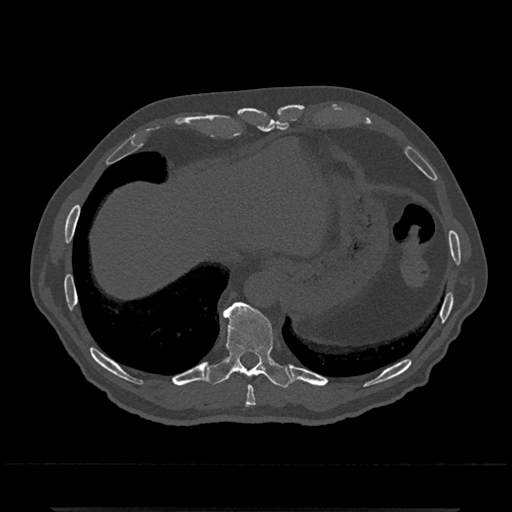
CT including the spine, one axial slice; reconstruction kernel Br40s/3; bone window (W 1800 / L 400 HU); 0.5 mm slice thickness; 512 × 512 image matrix, field of view 393 × 393 mm. Male patient, age 67 years. Case-level facts recorded for this patient, not image findings: primary cancer: prostate.
Structures marked on this image (semi-automatic segmentation, software-assisted and operator-edited):
- T10 vertebra: bounding box <205,302,292,388> (left, top, right, bottom; pixels)
- T9 vertebra: <245,386,256,407>